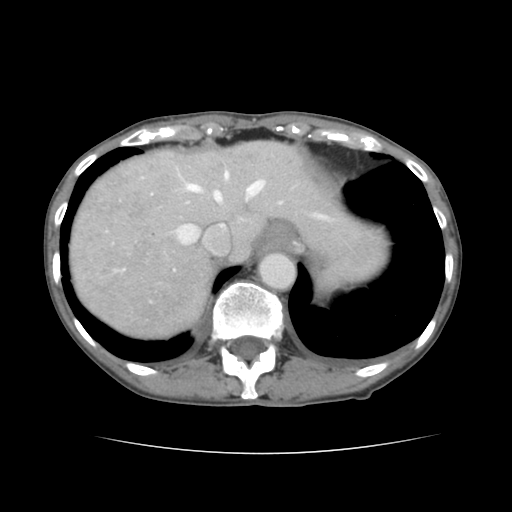
Contrast-enhanced abdominal CT, one axial slice; position 117 of 136 along the scan axis; 120 kVp; intravenous contrast given; soft-tissue window (W 400 / L 40 HU); 512 × 512 image matrix. Female patient, age 77 years. Case-level facts recorded for this patient, not image findings: diagnosis: colorectal cancer liver metastases, imaged before liver resection; multiple liver metastases: yes; largest metastasis: 3 cm; disease in both lobes: no.
Outlined on this slice (outlined manually by an expert reader):
- hepatic veins: bounding box (x1, y1, x2, y2) in pixels: (140, 172, 323, 253)
- liver: (71, 141, 376, 337)
- planned liver remnant (the part of the liver to remain after resection): (173, 141, 379, 257)